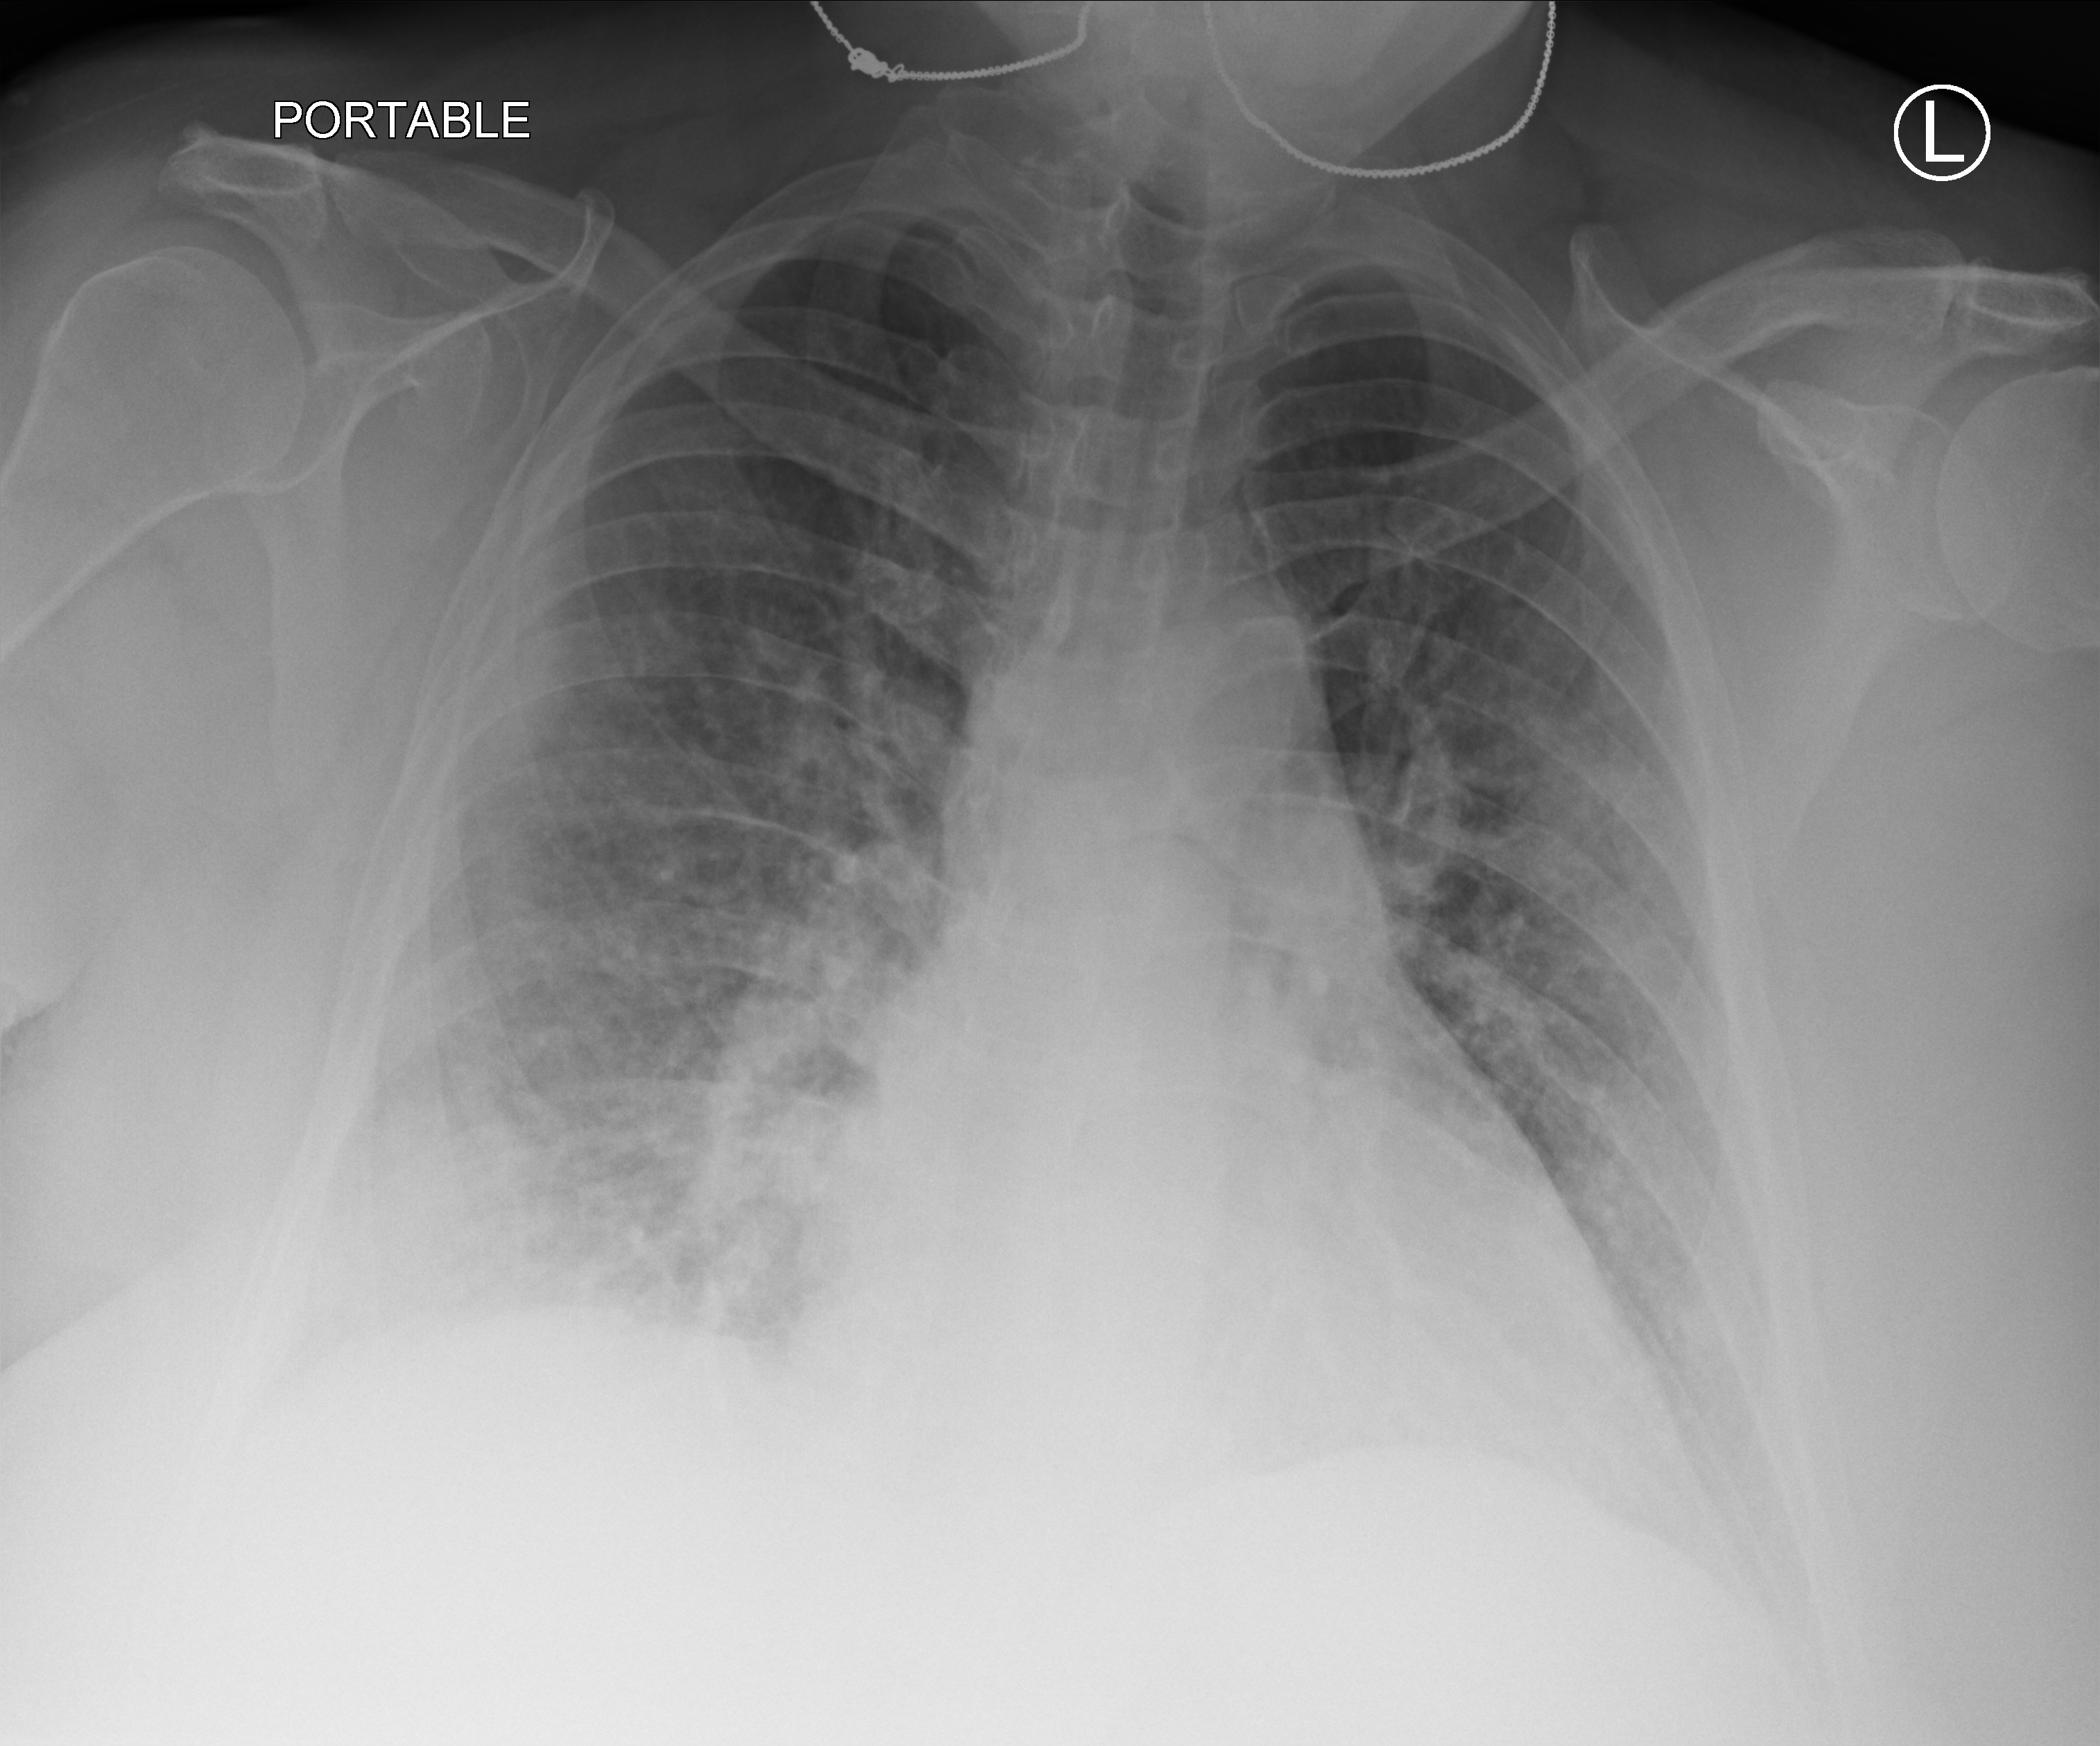
Chest X-ray (portable), anteroposterior (AP) projection. Female patient hospitalised with COVID-19, age 60–74 years.
Hospital-stay facts (about this admission, not read from this image; timing relative to this image not recorded):
- admitted to intensive care during this hospital stay: no
- length of hospital stay: 13 days
- mechanically ventilated during this hospital stay: no